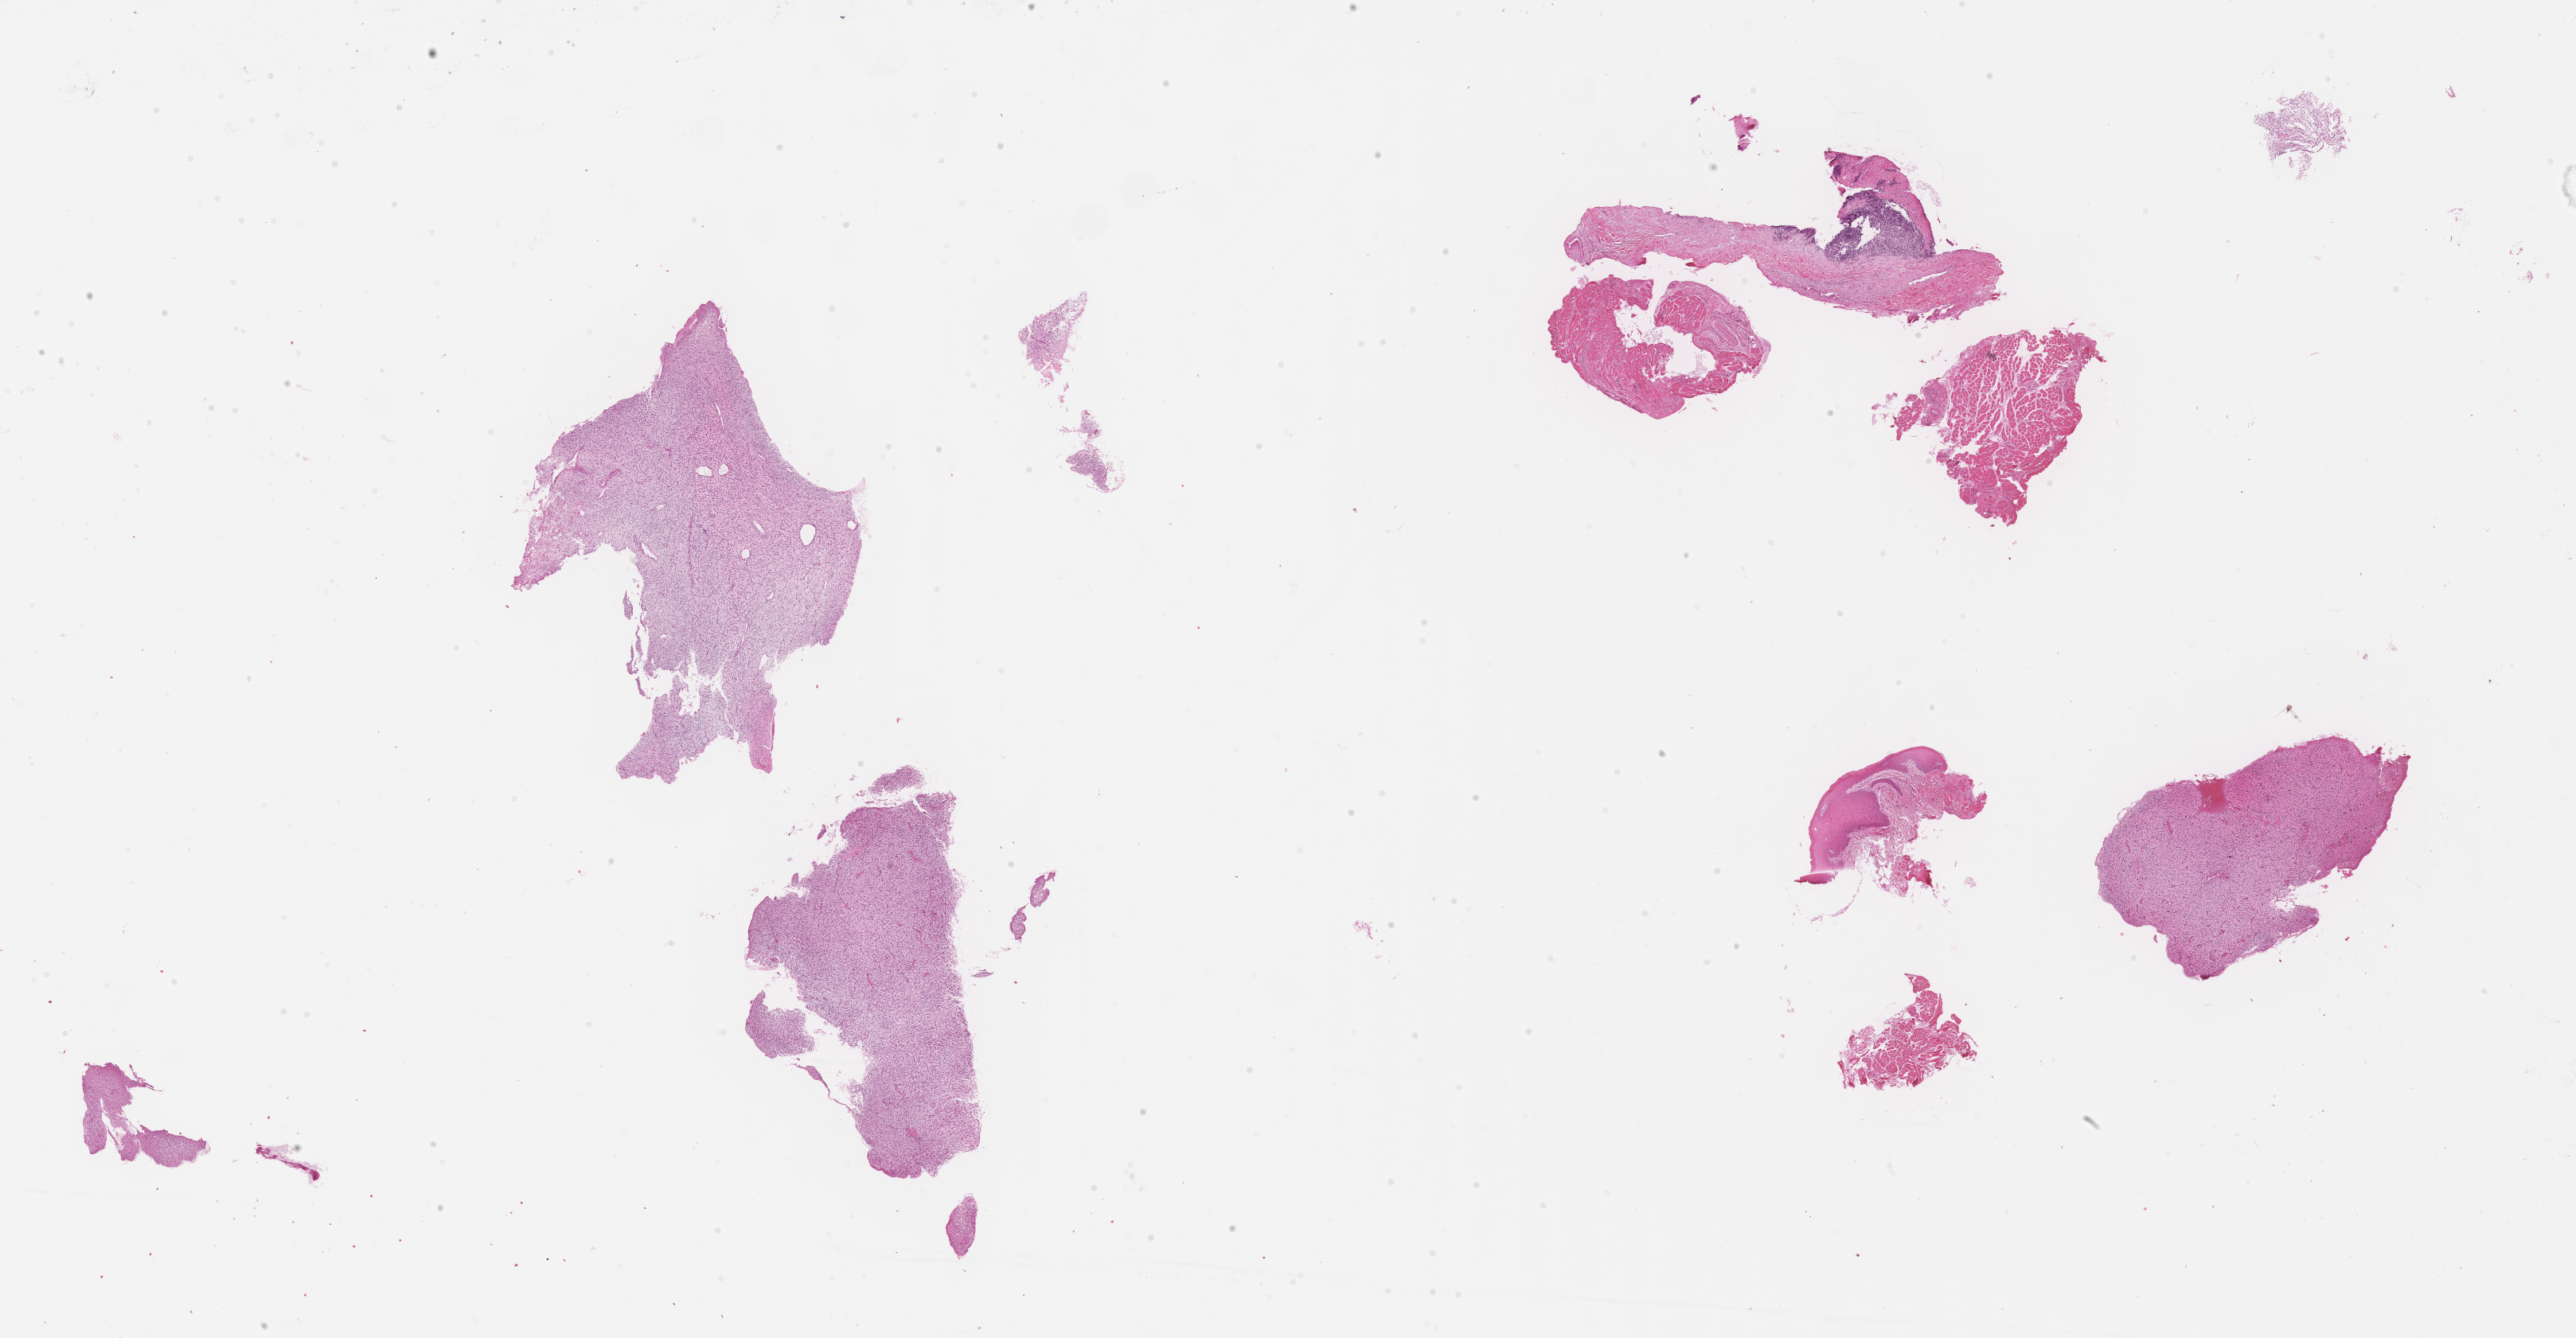
Whole-slide image, haematoxylin and eosin stain of tumor tissue — low-resolution overview of the scanned area, about 26.2 x 13.6 mm, FFPE section, site: soft tissue, mandible-left. Female patient, age at diagnosis 4.6 years.
Diagnosis: rhabdomyosarcoma; histological classification: embryonal rhabdomyosarcoma.